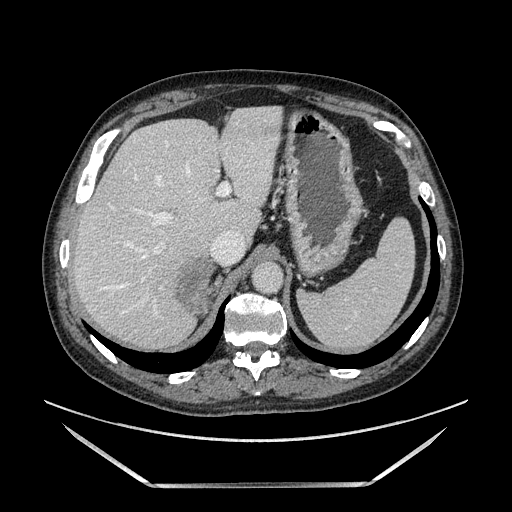
Contrast-enhanced abdominal CT, one axial slice. Soft-tissue window (W 400 / L 40 HU). 512 × 512 image matrix, field of view 440 × 440 mm. Male patient. From the clinical record (not read from this slice): diagnosis: adrenocortical carcinoma; tumour side: right adrenal; tumour size at pathology: 10.3 cm; Ki-67 index: 20 %; stage (as recorded): 3.
Structures marked on this image (semi-automatic segmentation, software-assisted and operator-edited):
- mass: box from (x=178, y=260) to (x=213, y=310) px